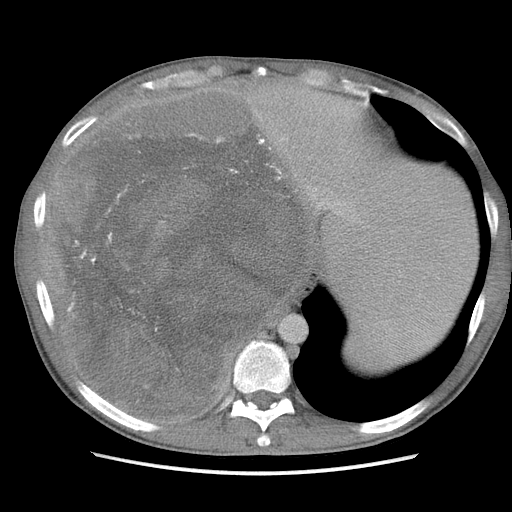
Contrast-enhanced abdominal CT, one axial slice; slice 87 of 115 in the series (ordered by position); soft-tissue window (W 400 / L 40 HU); 5 mm slice thickness; 512 × 512 image matrix, field of view 360 × 360 mm. Male patient. From the clinical record (not read from this slice): diagnosis: adrenocortical carcinoma; tumour side: right adrenal.
Structures marked on this image (semi-automatic segmentation, software-assisted and operator-edited):
- mass: box from (x=66, y=91) to (x=299, y=416) px